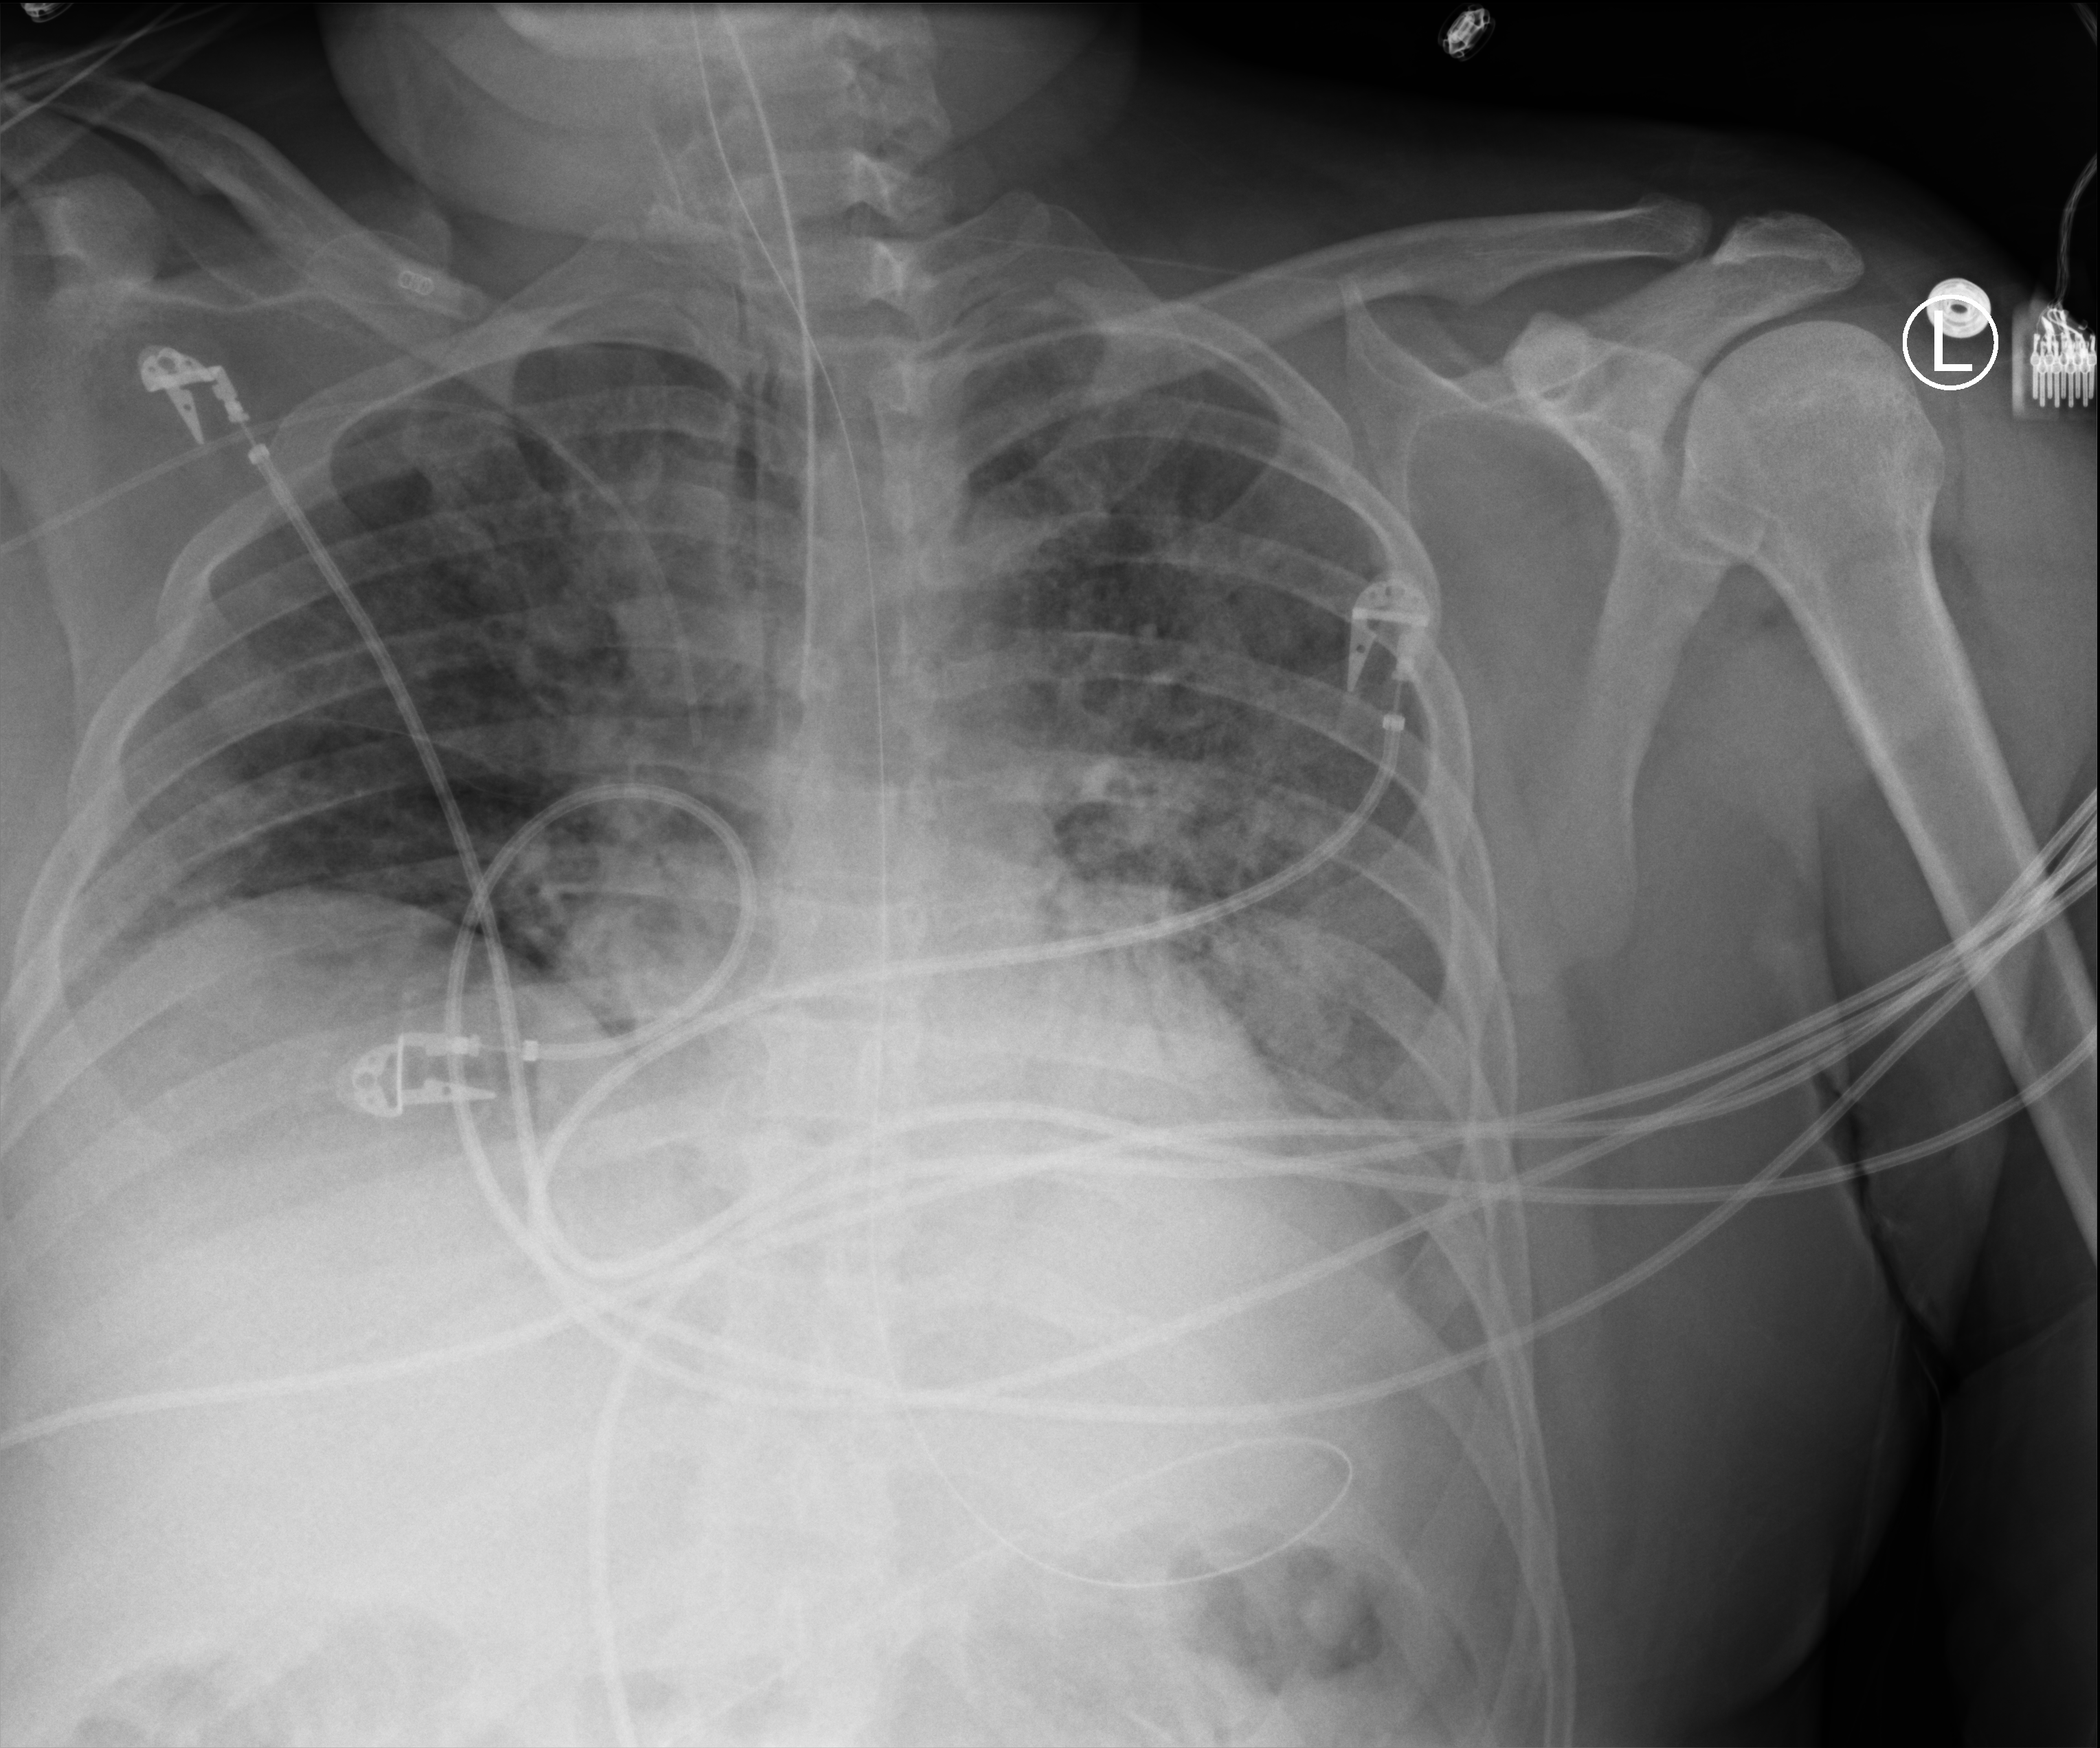
Portable chest radiograph; anteroposterior (AP) projection. Patient hospitalised with COVID-19; male, aged 18–59 years.
From the hospital-stay record, not from the radiograph (when in the stay this image was taken is not recorded):
- admitted to intensive care during this hospital stay: yes
- smoking status (admission record): never